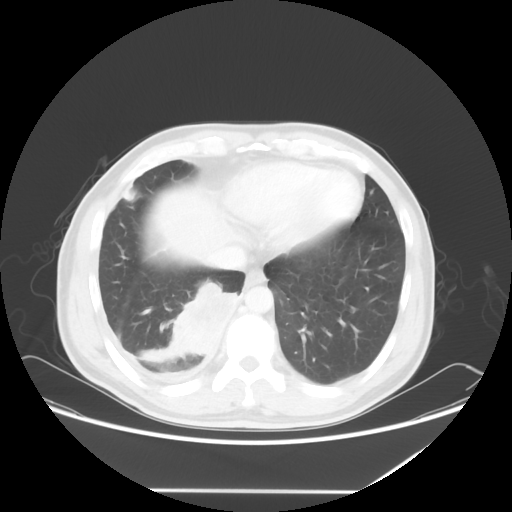
Chest CT, one axial slice; slice 18 of 60 in the series (ordered by position); 120 kVp; lung window (W 1500 / L -600 HU); 5 mm slice thickness; 512 × 512 image matrix, field of view 419 × 419 mm. Patient: male, 48 years. Case-level facts recorded for this patient, not image findings: clinical TNM (as recorded): T3 N3 M1a.
Annotated regions visible in this slice (rectangle marked by the reading radiologist):
- lung tumour (recorded histology: squamous cell carcinoma): bounding box <165,273,243,360> (left, top, right, bottom; pixels)